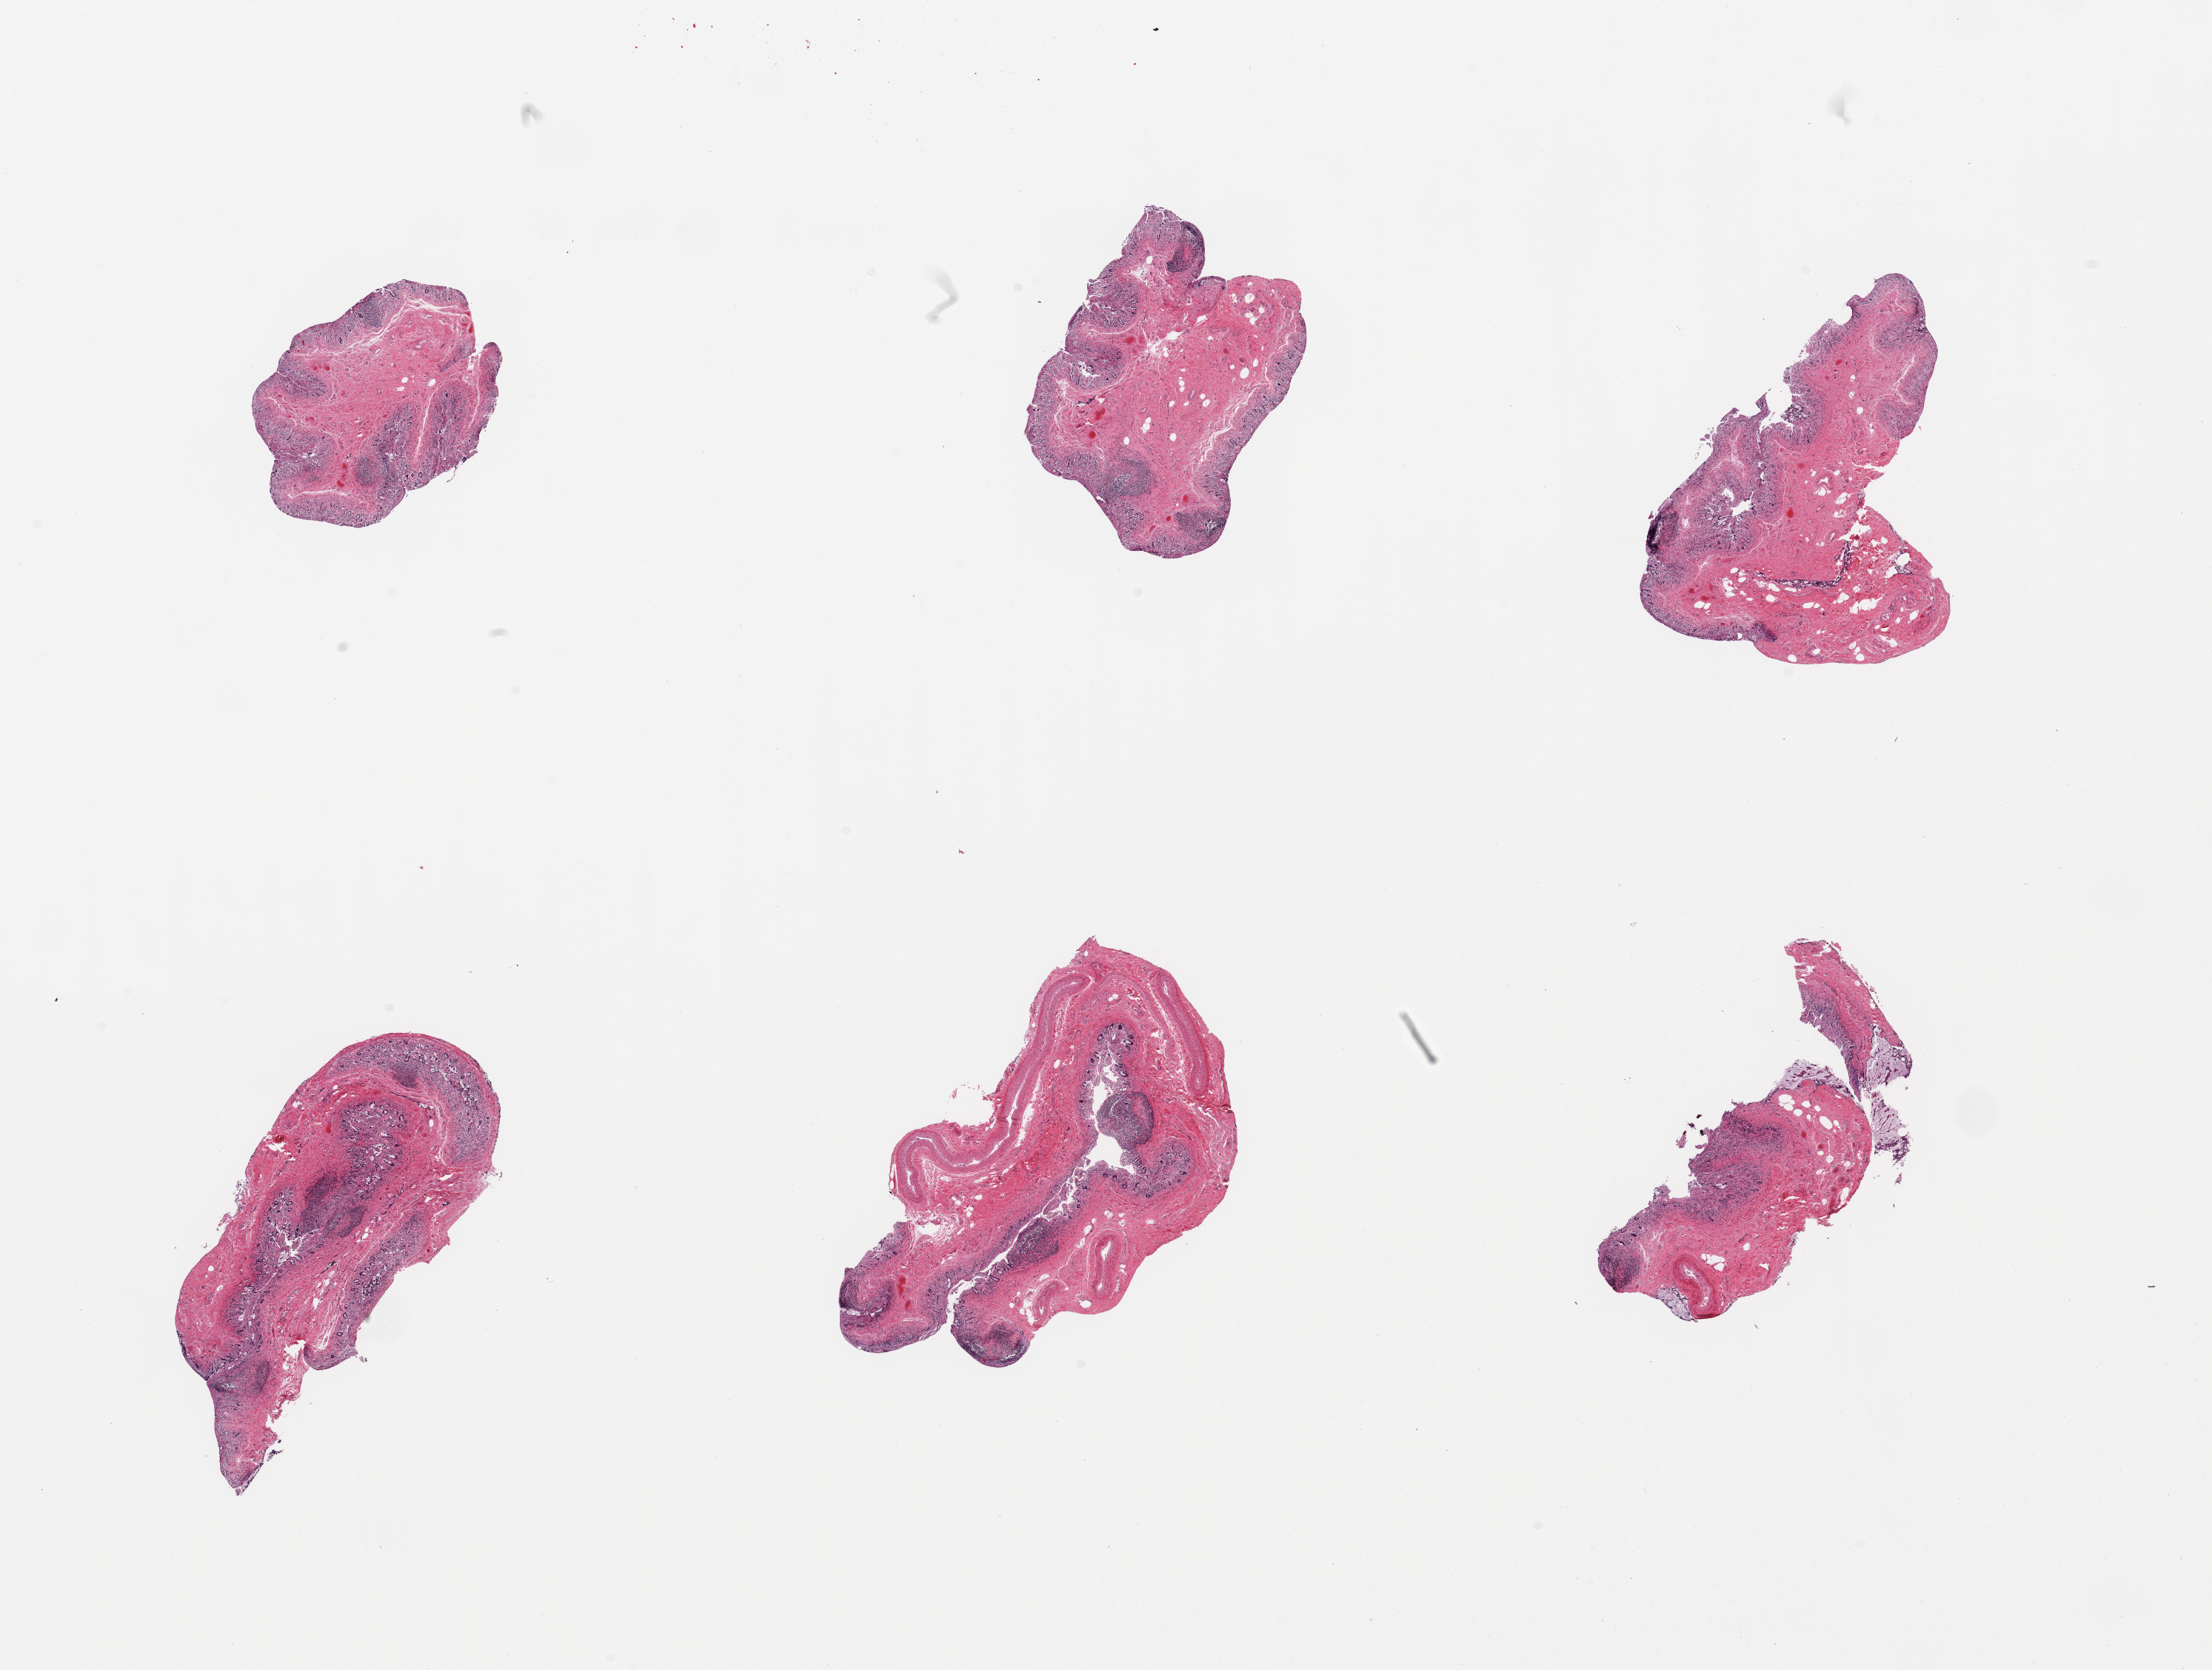
Whole-slide image, haematoxylin and eosin stain — whole scanned area (about 23.6 x 17.8 mm) shown as a low-resolution overview. PAXgene-fixed paraffin-embedded (PFPE) section. Section of ileum (target tissue). Donor tissue sample. Male donor.
Reviewer comment on this tissue sample: 6 pieces, advanced mucosal autolysis, <1% target lymphoid aggregates remain.